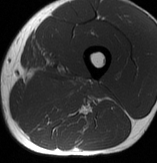
MRI of an extremity soft-tissue mass, one axial slice; slice 27 of 70 in the series (ordered by position); MR volume resampled by the dataset authors to the PET/CT grid (not the native acquisition matrix); 157 × 163 image matrix, field of view 153 × 159 mm. Male patient. From the clinical record (not read from this slice): histological type: extraskeletal osteosarcoma; grade: high; site of the primary tumour: left adductur.
Annotated regions visible in this slice (expert contour drawn on MRI and transferred to this co-registered scan by the dataset authors):
- gross tumour volume (mass): bounding box [x1, y1, x2, y2] px = [24, 74, 109, 127]